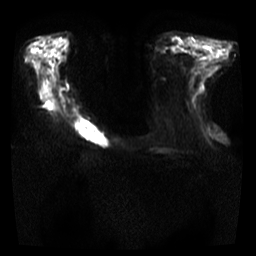
Breast MRI, one axial slice. Slice 12 of 35 in the series (ordered by position). Diffusion-weighted series; image 2 of 4 stored at this slice position (different b-values; order by instance number). 3 T. 5 mm slice thickness. 256 × 256 image matrix. Female patient.
Structures marked on this image (expert manual segmentation):
- tumour on diffusion-weighted imaging: bounding box (x1, y1, x2, y2) in pixels: (75, 121, 108, 147)